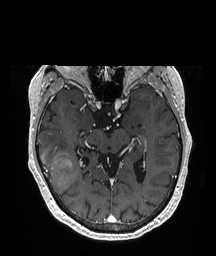
Brain MRI from a brain-tumour surgery series, one axial slice. Slice 123 of 208 in the series (ordered by position). T1-weighted post-contrast. 1 mm slice thickness. 216 × 256 image matrix. Case-level facts recorded for this patient, not image findings: histopathology: Glioblastoma; WHO grade: 4; IDH mutation: no; tumour location: Right Temporal.
Structures marked on this image (manually delineated by an expert):
- tumour: bounding box [x1, y1, x2, y2] px = [39, 150, 78, 195]